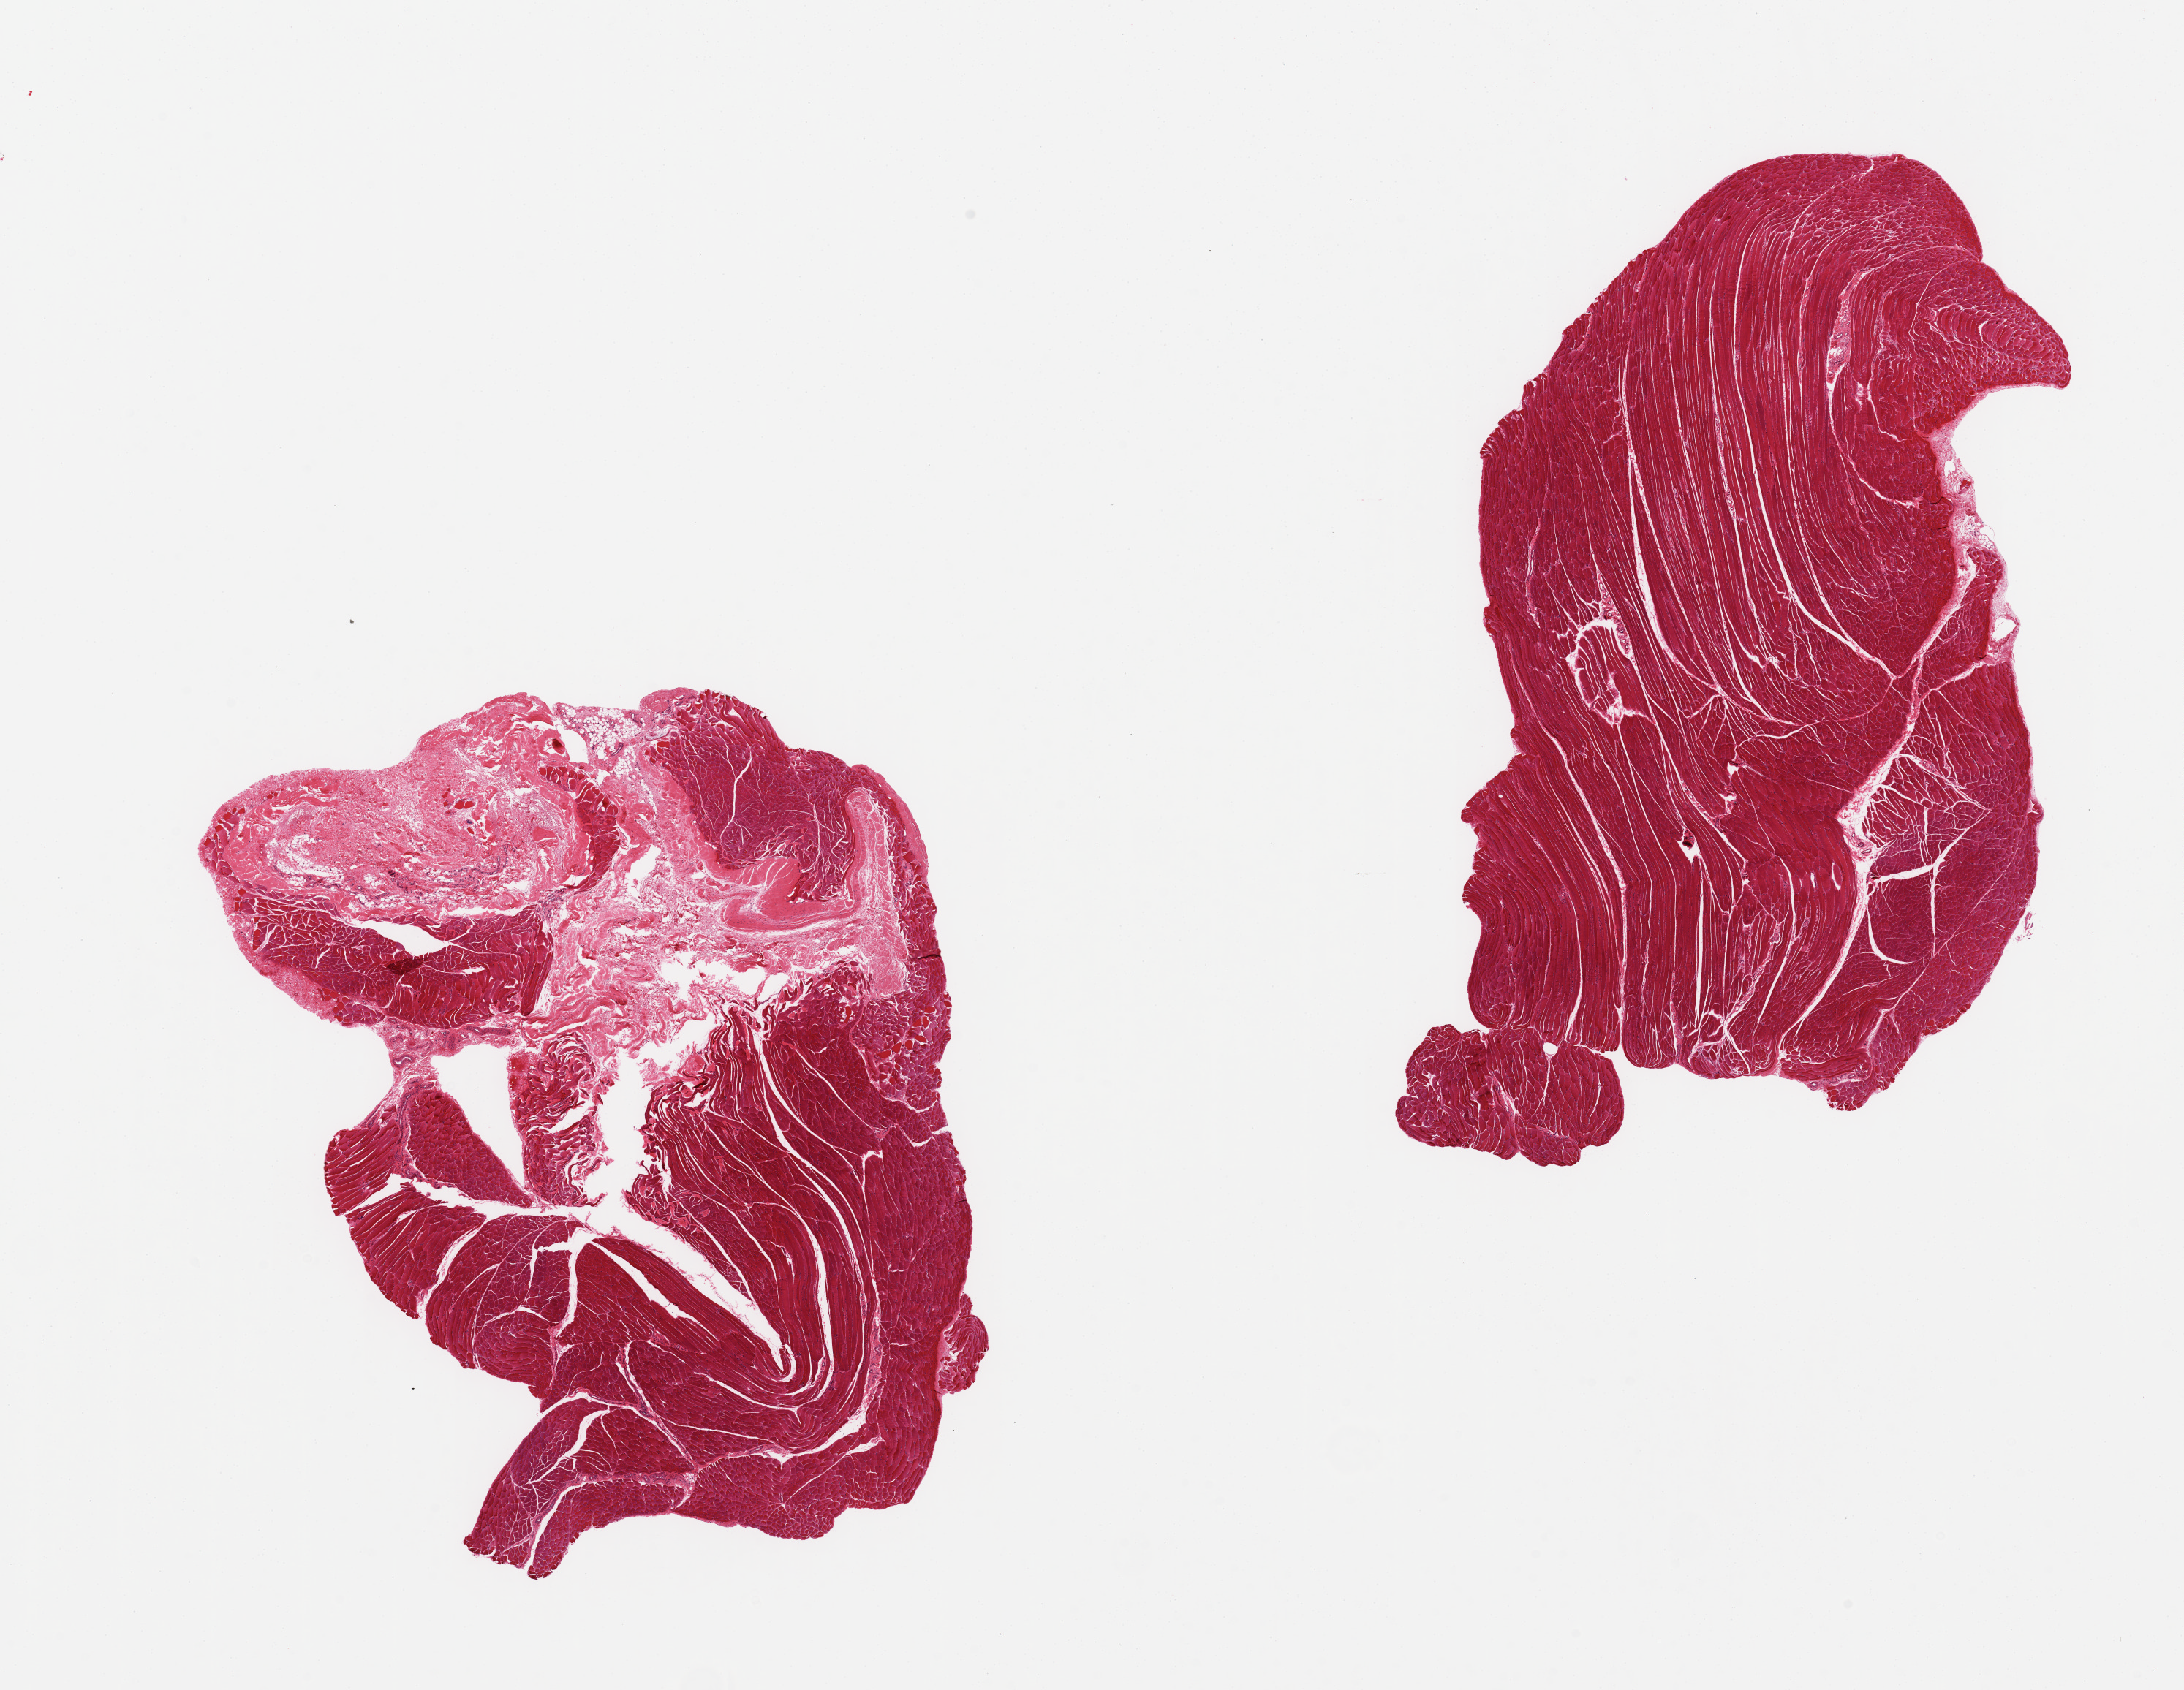
Haematoxylin and eosin whole-slide image, whole scanned area (about 23.6 x 18.3 mm) shown as a low-resolution overview; PAXgene-fixed, paraffin-embedded tissue; section of skeletal muscle (target tissue); donor tissue sample. Male donor.
Reviewer comment on this tissue sample: 2 pieces, 1 with 40% fibrous tissue.